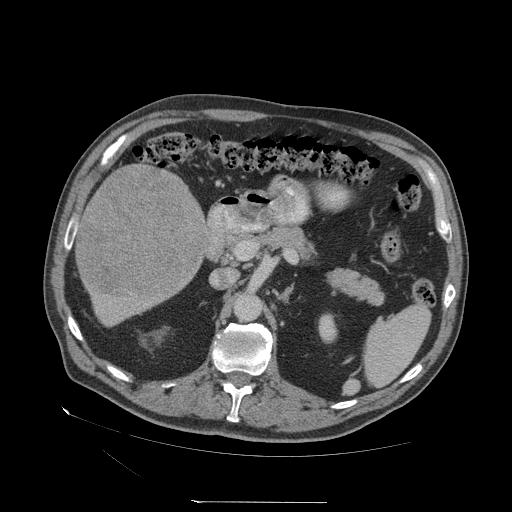
Contrast-enhanced abdominal CT (liver protocol), one axial slice; position 20 of 83 along the scan axis; soft-tissue window (W 400 / L 40 HU); 2.5 mm slice thickness; 512 × 512 image matrix. From the clinical record (not read from this slice): diagnosis: hepatocellular carcinoma (patient treated with transarterial chemoembolisation; whether this scan precedes or follows treatment is not stated here); TNM stage (as recorded): Stage-I; Child-Pugh class: A; tumour nodularity: uninodular.
Outlined on this slice (semi-automatic segmentation, software-assisted and operator-edited):
- liver parenchyma outside the tumour (the mass and vessels are separate outlines, so this box may not span the whole liver): bounding box <76,164,208,324> (left, top, right, bottom; pixels)
- mass: <76,164,205,298>